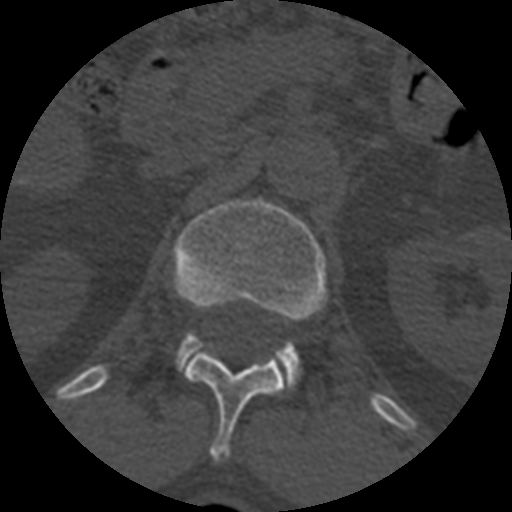
CT including the spine, one axial slice. Reconstruction kernel STANDARD. 120 kVp. Bone window (W 1800 / L 400 HU). 1.25 mm slice thickness. 512 × 512 image matrix, field of view 160 × 160 mm. Patient age 71 years. From the clinical record (not read from this slice): primary cancer: prostate.
Structures marked on this image (semi-automatic segmentation, software-assisted and operator-edited):
- L1 vertebra: bounding box [x1, y1, x2, y2] px = [173, 199, 325, 389]
- T12 vertebra: [183, 348, 286, 461]